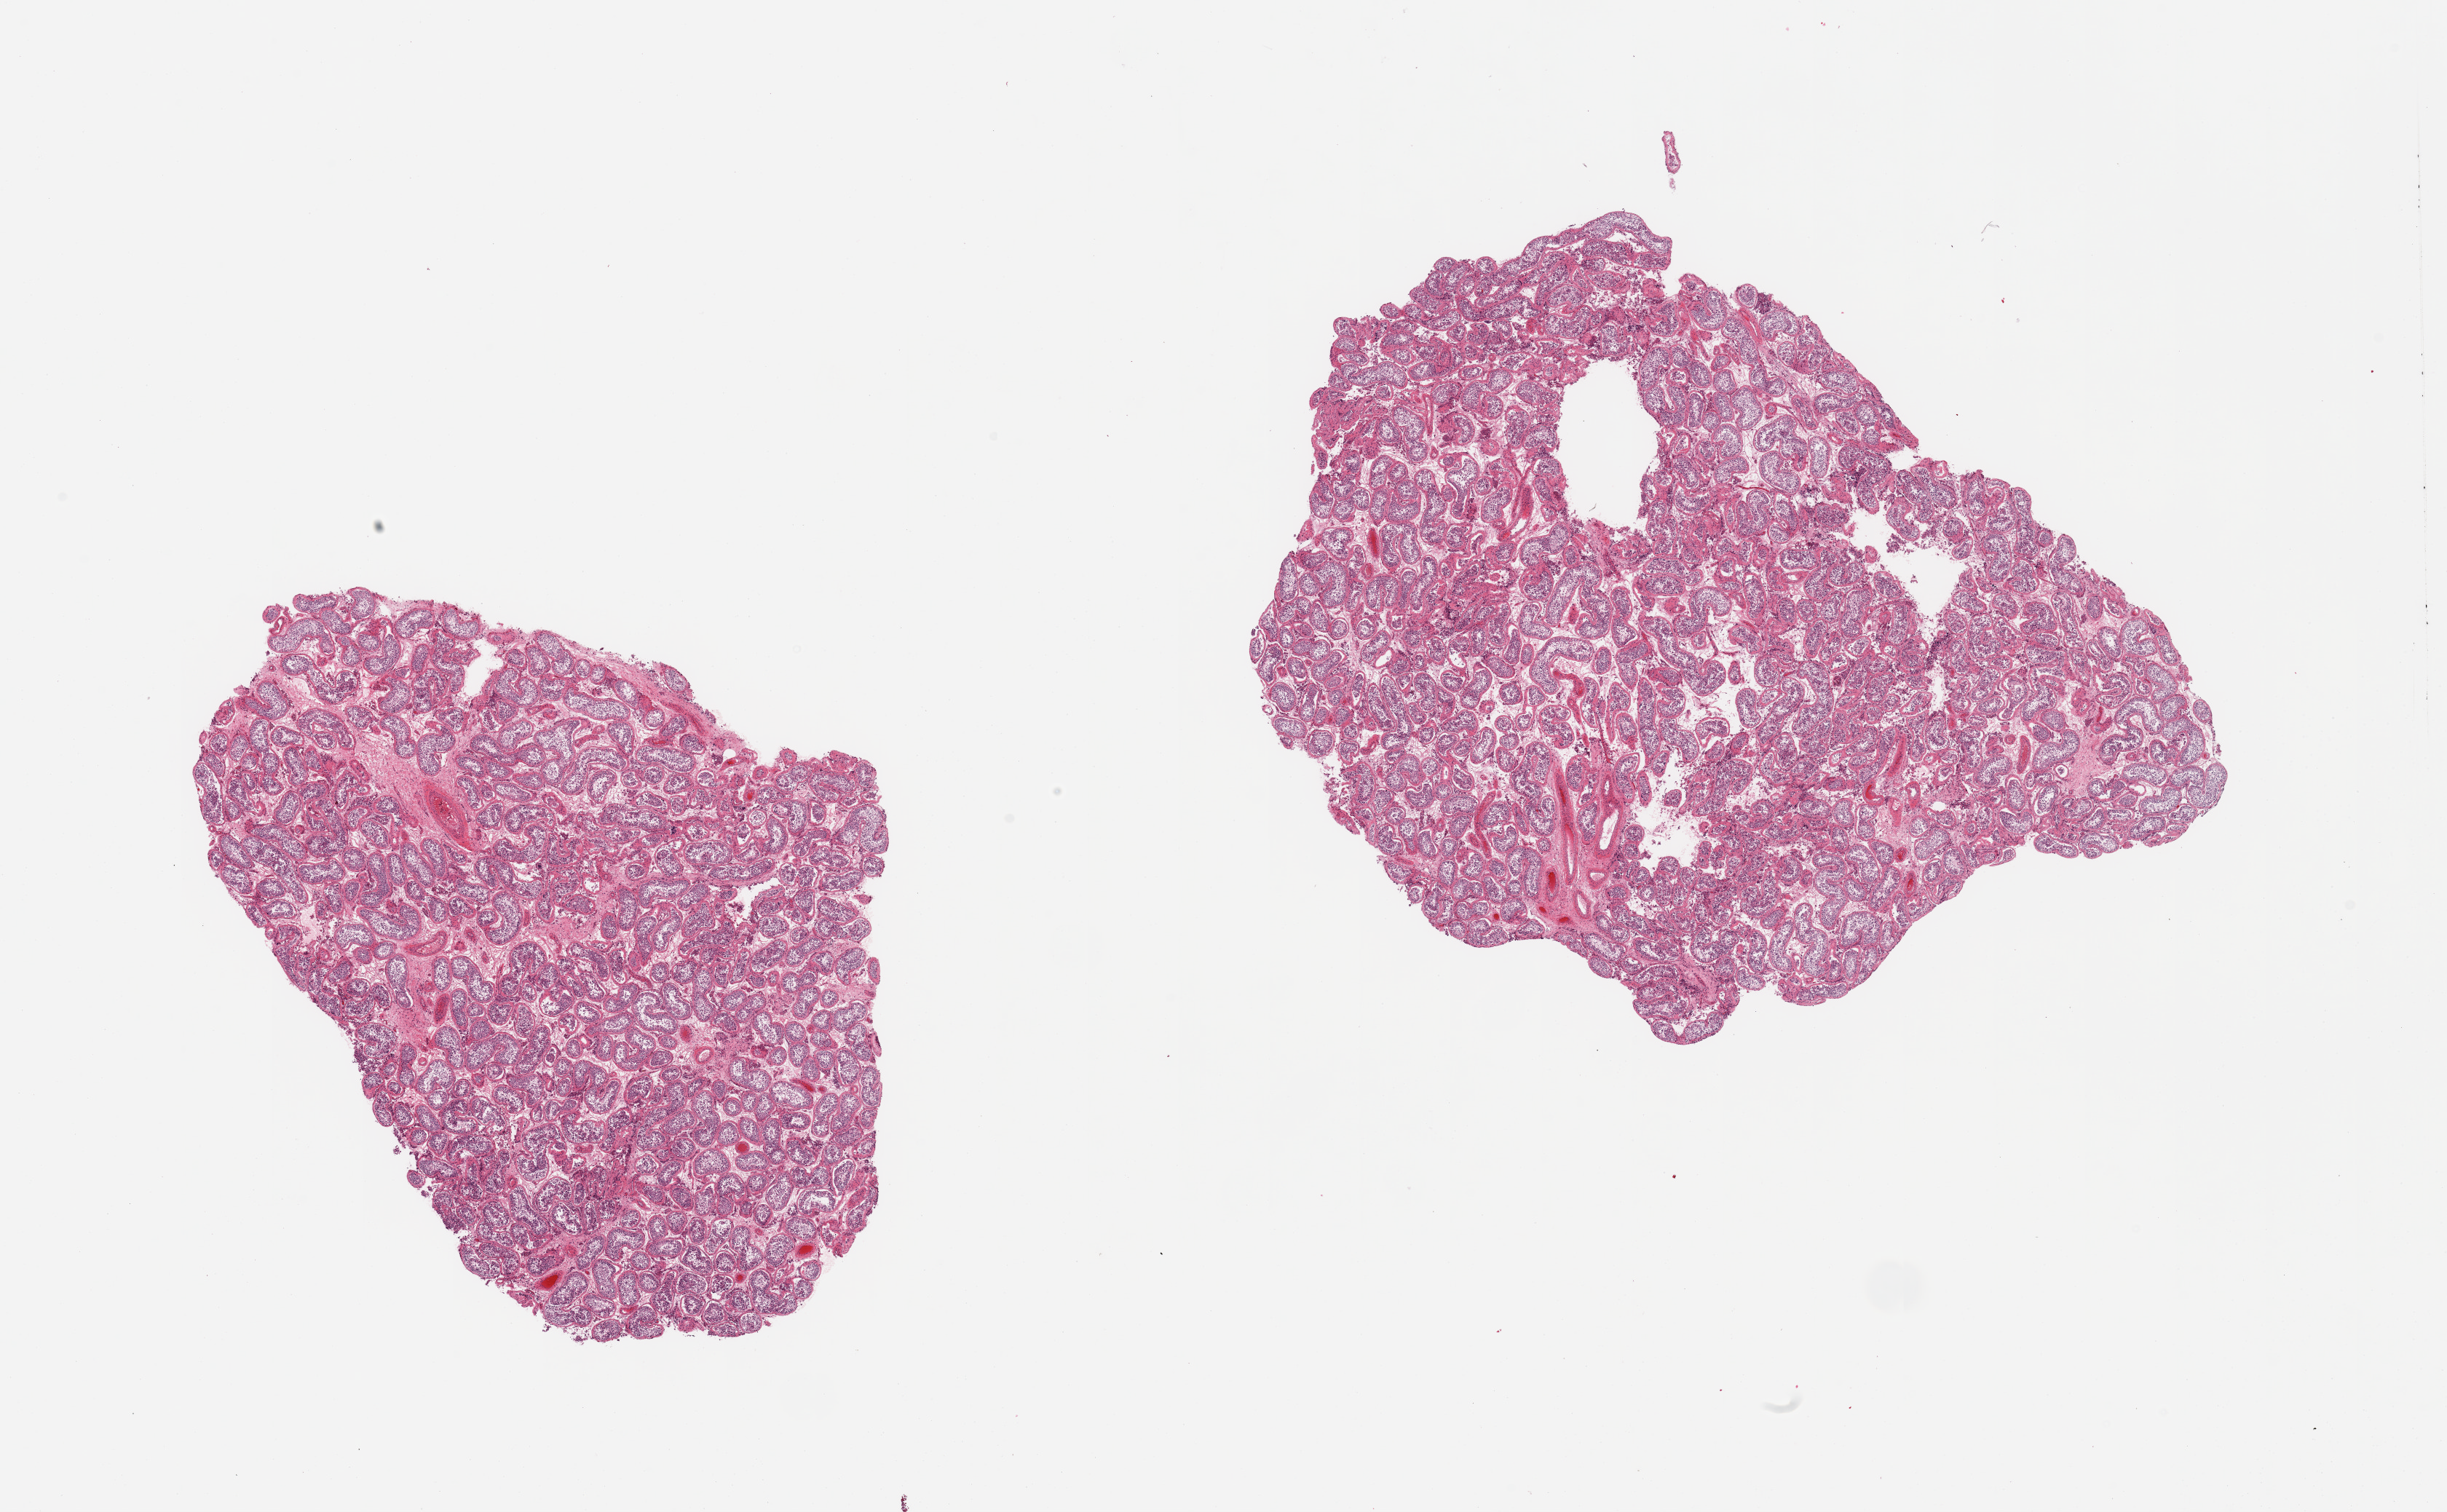
Hematoxylin and eosin (H&E) whole-slide image — a low-resolution overview of the entire scanned area, about 26.6 x 16.4 mm (slide scanned at 20x), PAXgene-fixed paraffin-embedded (PFPE) section, sampled site (target tissue): testis, donor tissue sample. Male donor.
- review note (as recorded): 2 pieces; spermatogenesis